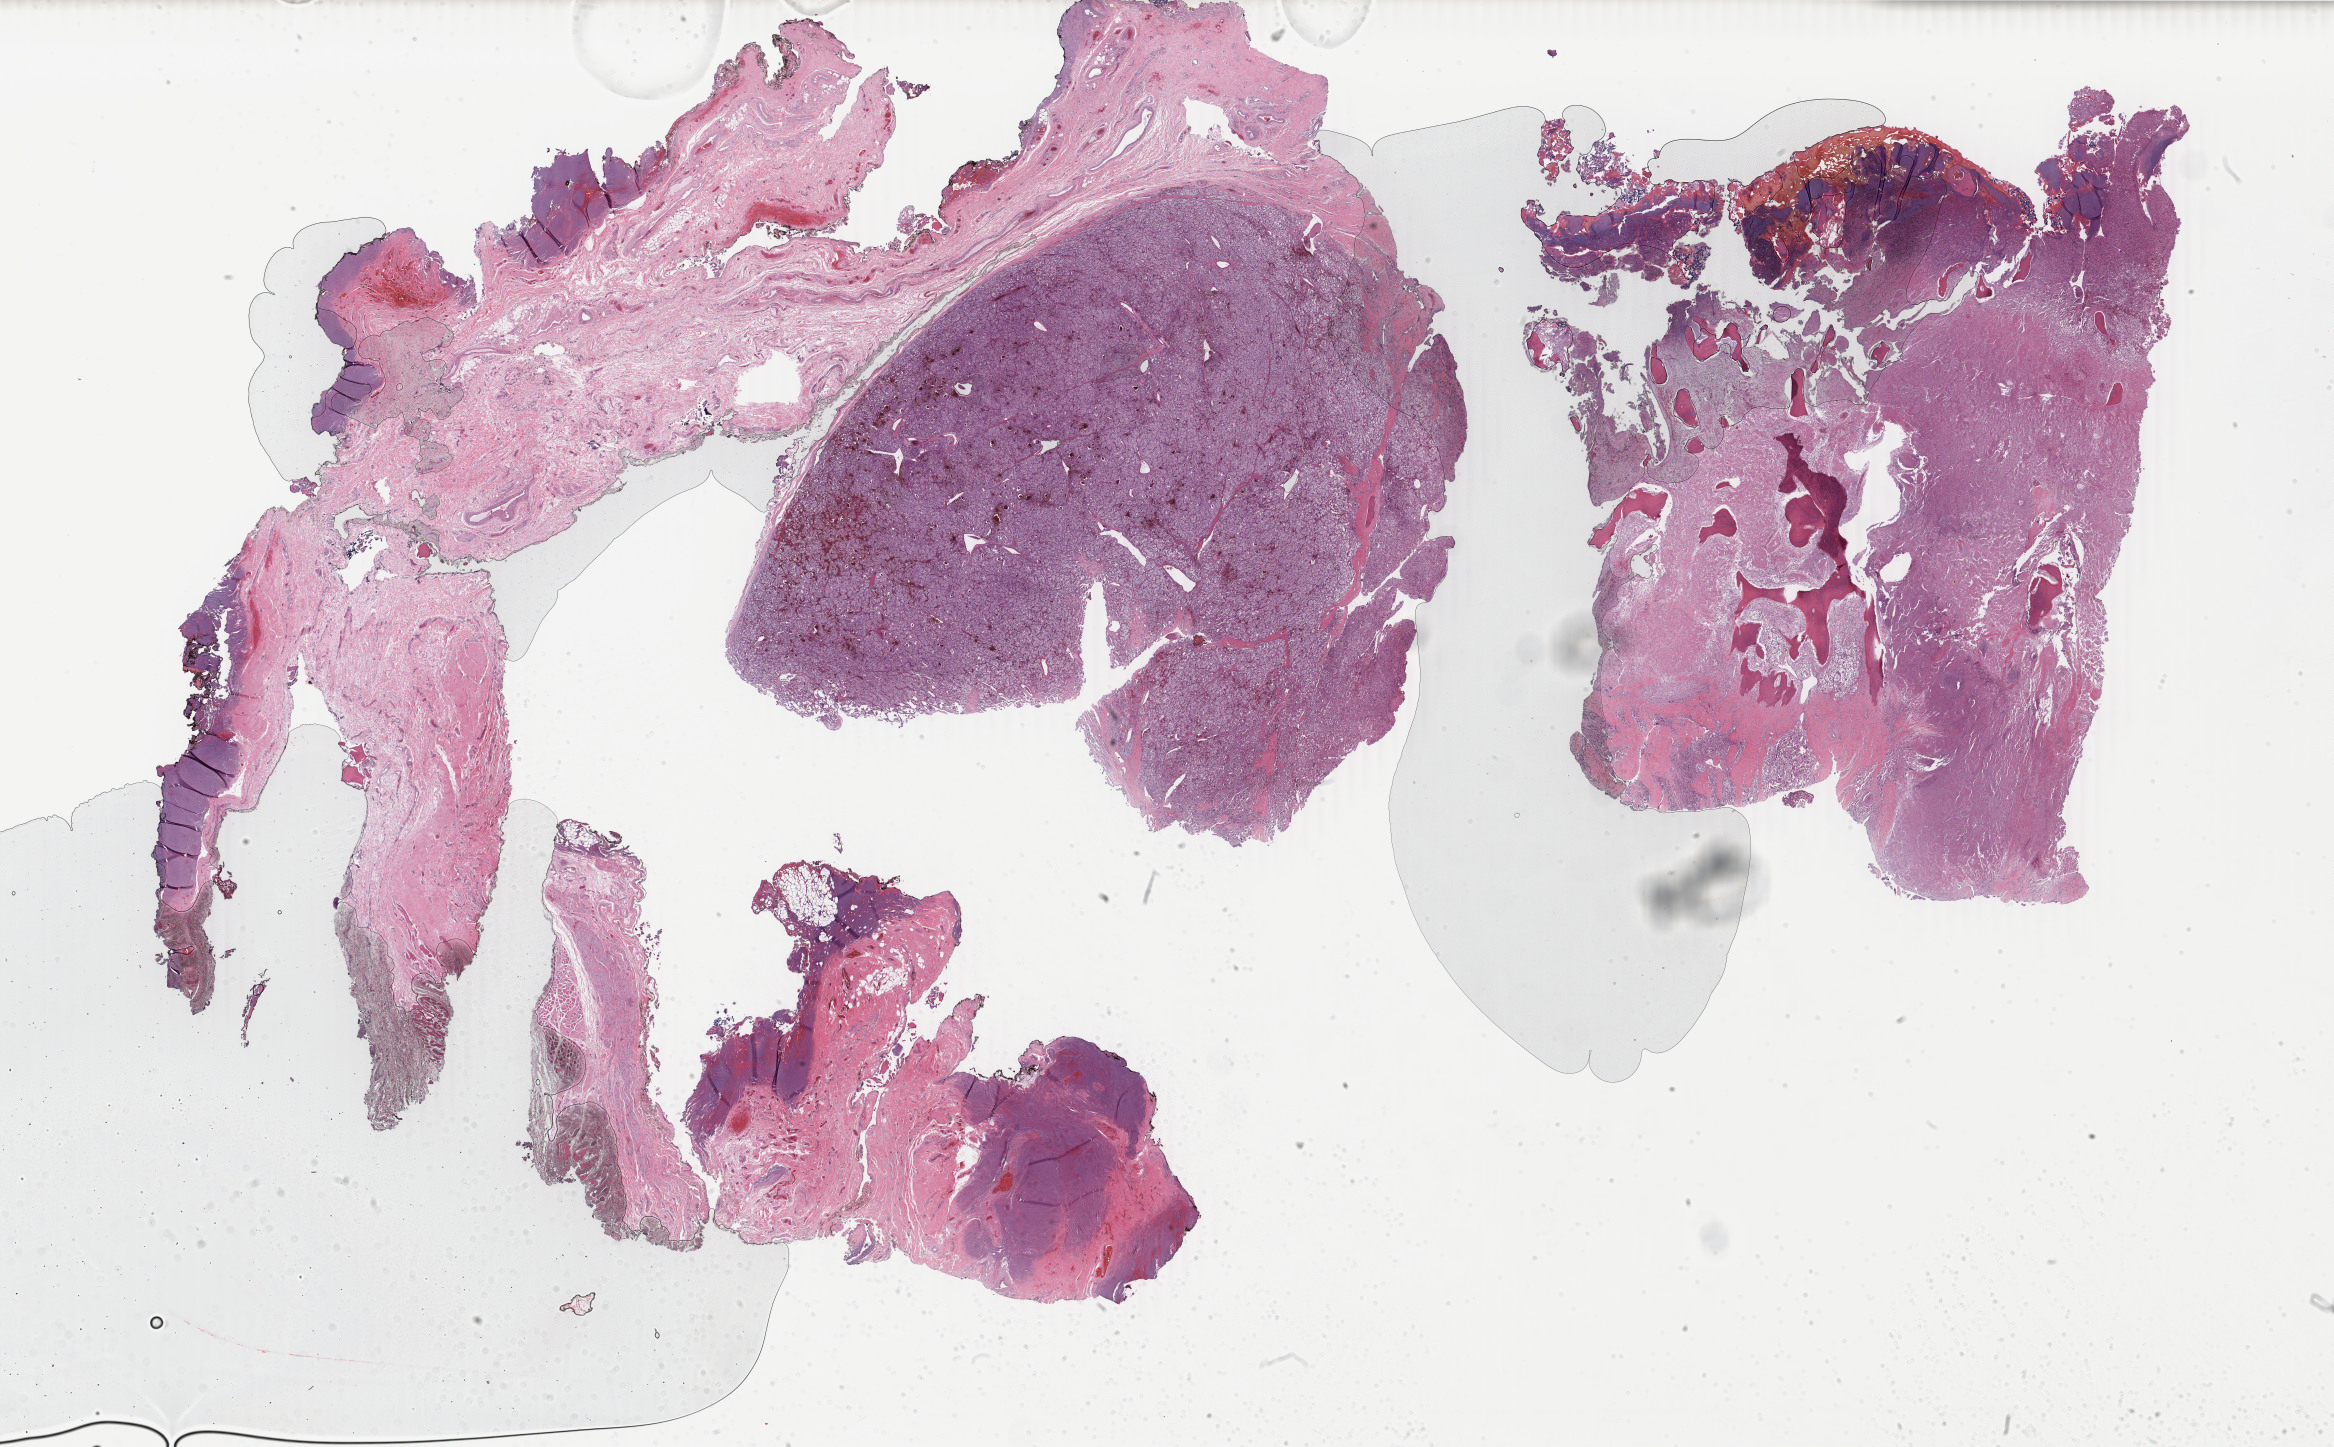
Whole-slide histology image, H&E — low-resolution overview of the scanned area, about 37.1 x 23.0 mm. FFPE section. Metastatic tumour sample, sampled site not recorded. Male, age 55 years at initial diagnosis.
This section: metastatic tumour tissue. Patient diagnosis: Paraganglioma, malignant (primary site: nervous system, NOS).